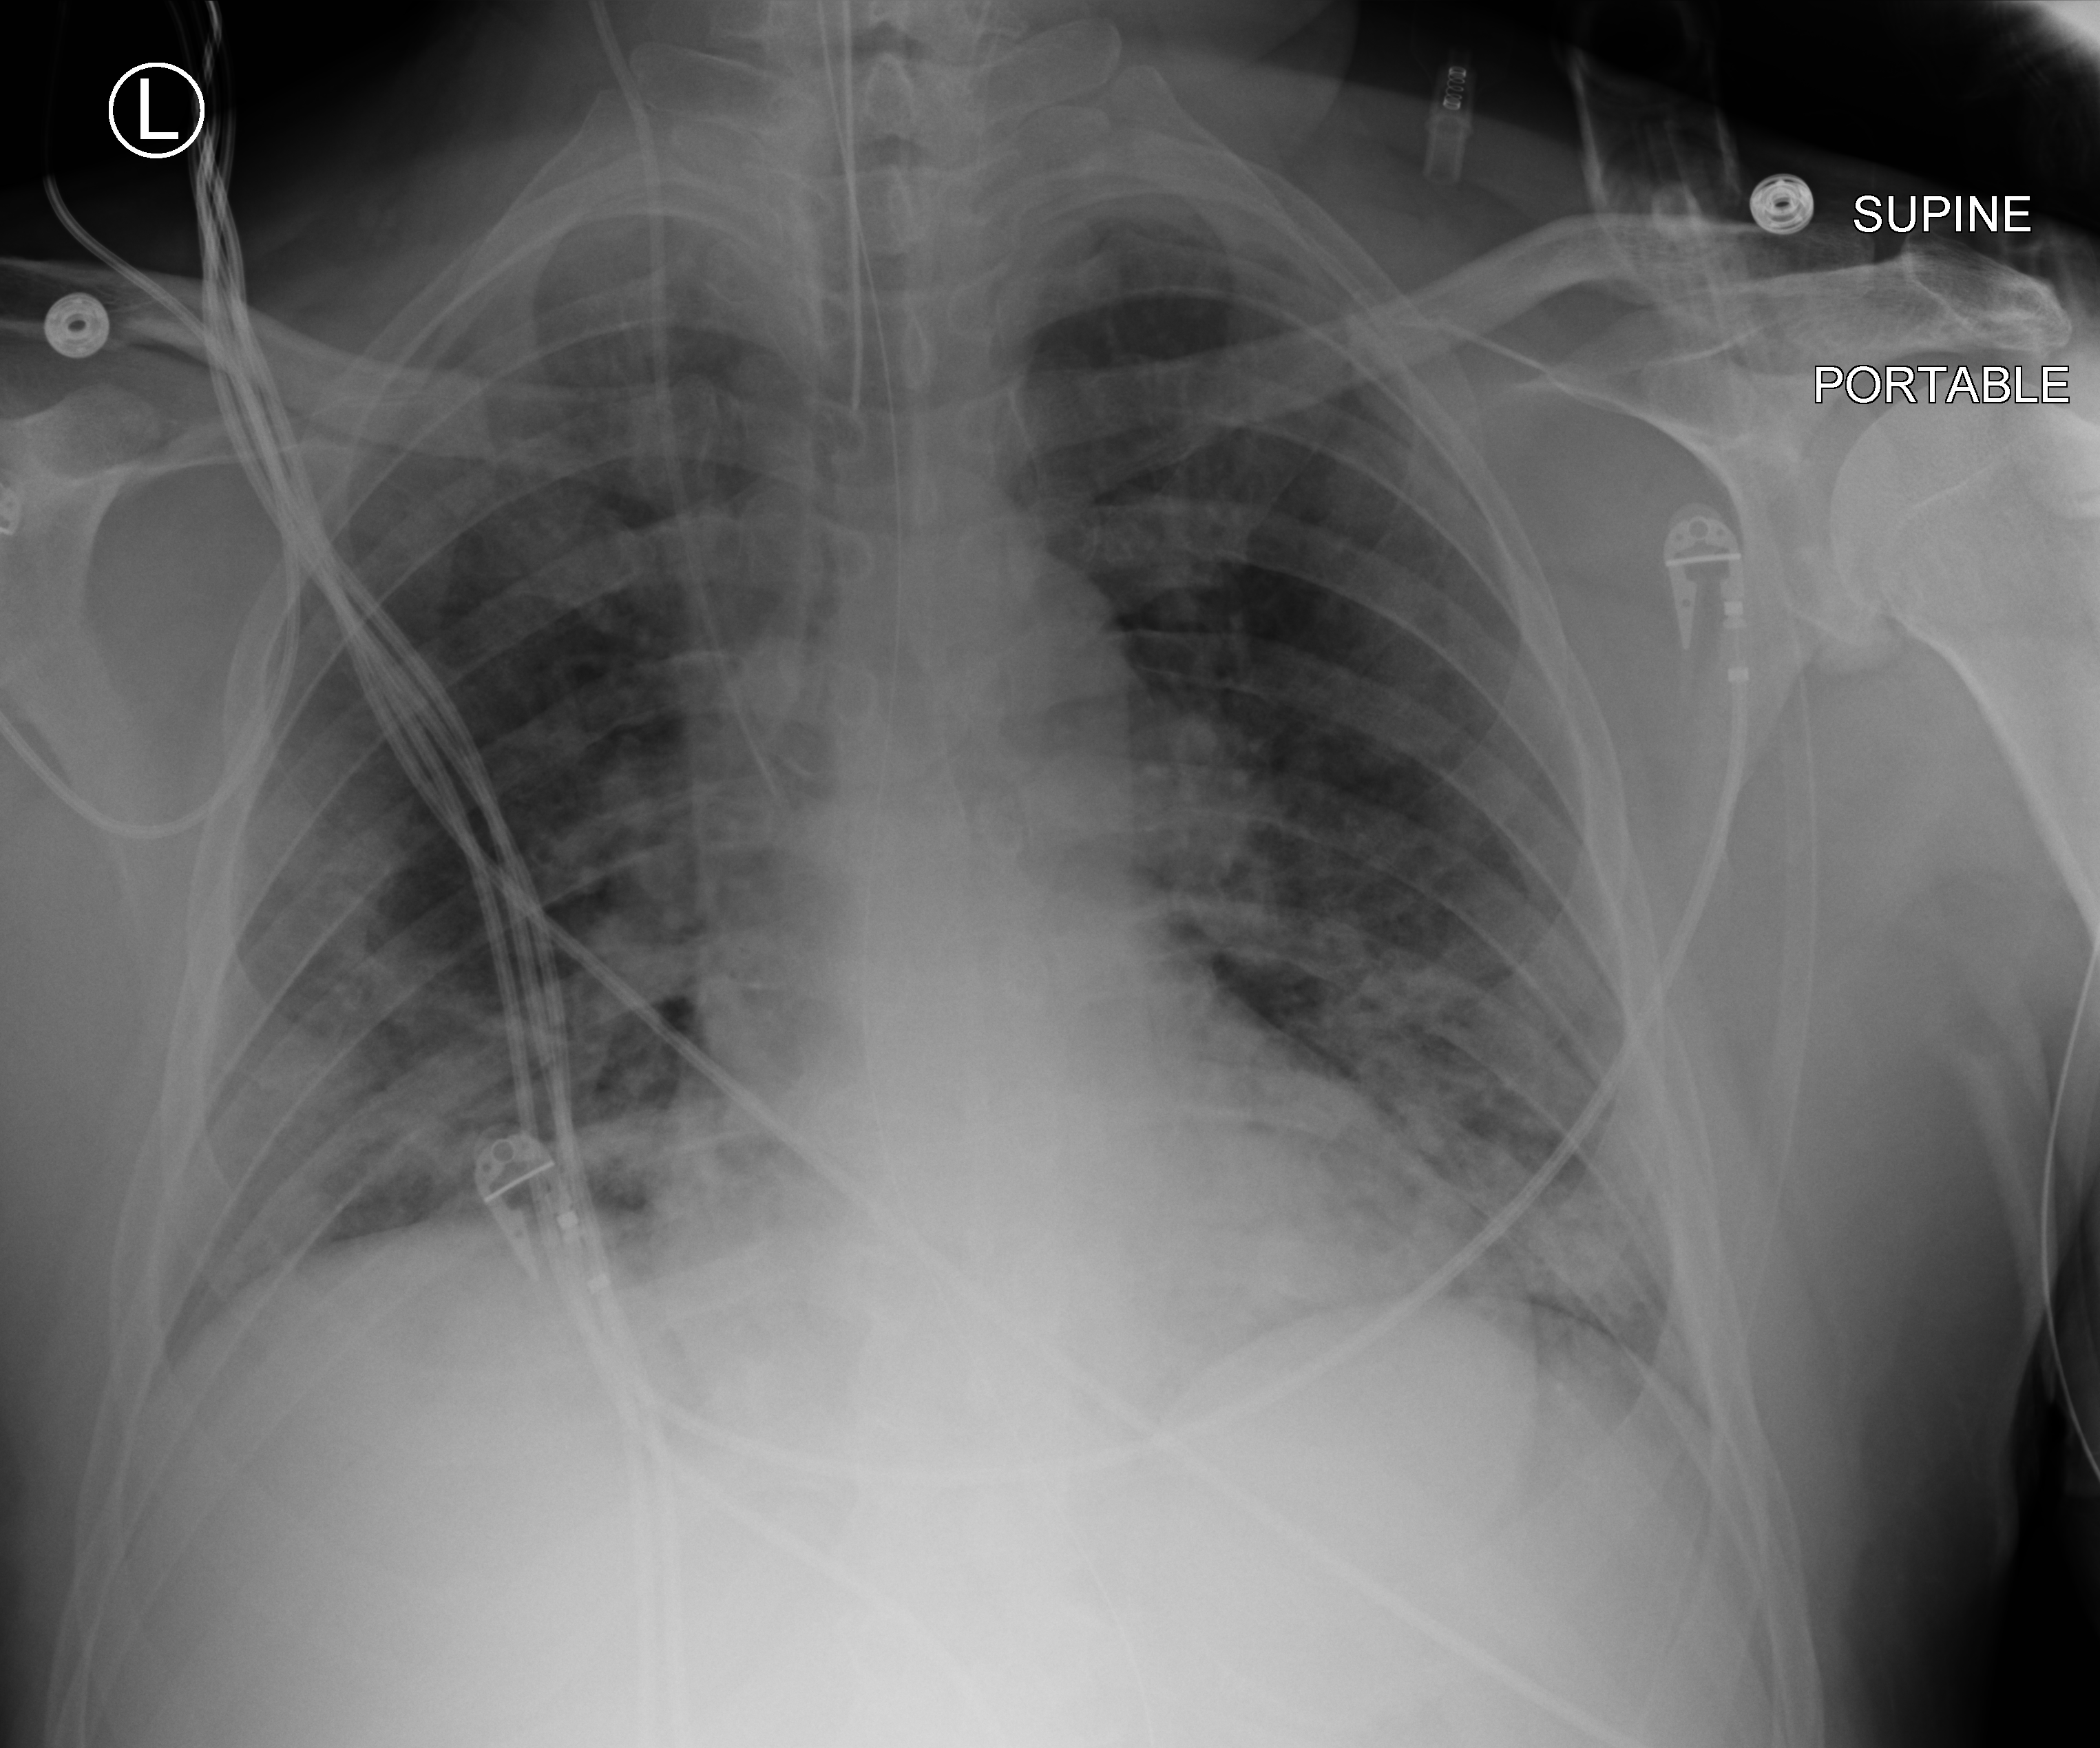
Chest X-ray (portable); anteroposterior (AP) projection. Male patient hospitalised with COVID-19, age 18–59 years.
Admission-level facts for this patient (not findings on this image; timing relative to this image not recorded):
- mechanically ventilated during this hospital stay: yes
- length of hospital stay: 32 days
- admitted to intensive care during this hospital stay: no